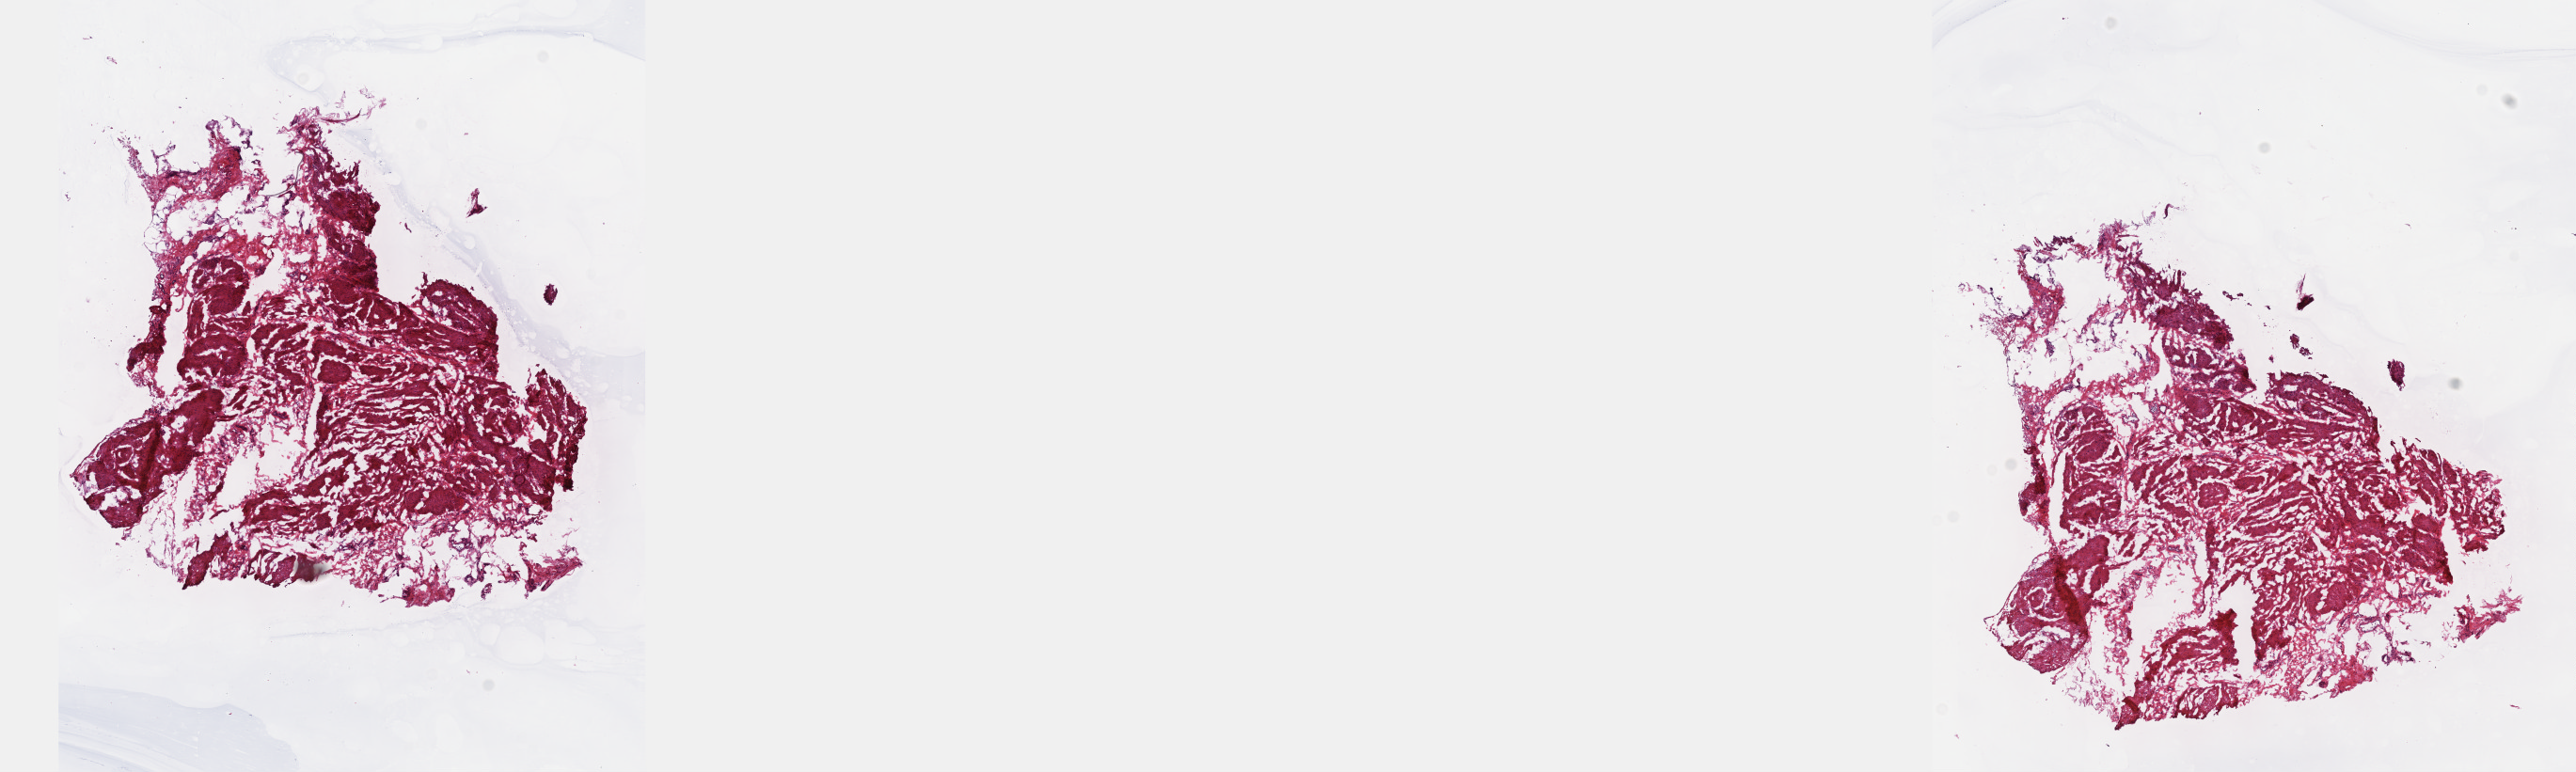
H&E-stained whole-slide image — low-resolution overview of the scanned area, about 22.1 x 6.6 mm; frozen section from the top of the tissue portion; solid tissue normal (non-tumour tissue) sample from the bladder. Female, age 78 years at initial diagnosis. Pathologist review of this section (percent, as recorded): tumour cells 0%, tumour nuclei 0%.
This section: solid tissue normal (non-tumour) sample from the same patient. Patient diagnosis: Transitional cell carcinoma.